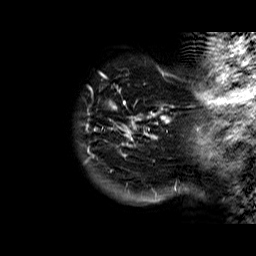
Breast MRI (dynamic contrast-enhanced), one sagittal slice. Position 3 of 60 along the scan axis. Dynamic contrast-enhanced series, time point 2 of 6 at this slice position (early post-contrast). 1.5 T. TE 6.3 ms, TR 32.4 ms. 4 mm slice thickness. 256 × 256 image matrix. Female patient. Case-level facts recorded for this patient, not image findings: setting: breast cancer imaged before/during neoadjuvant chemotherapy; receptor status: HR-positive, HER2-negative.
Annotated regions visible in this slice (semi-automatically segmented with operator editing):
- analysis volume of interest (the breast-tissue region the enhancement analysis was run in; not a lesion): box from (x=81, y=72) to (x=175, y=183) px
- tumour enhancement mask (voxels above the 100 % enhancement threshold inside the analysis volume of interest): (x=86, y=73)–(x=170, y=156)